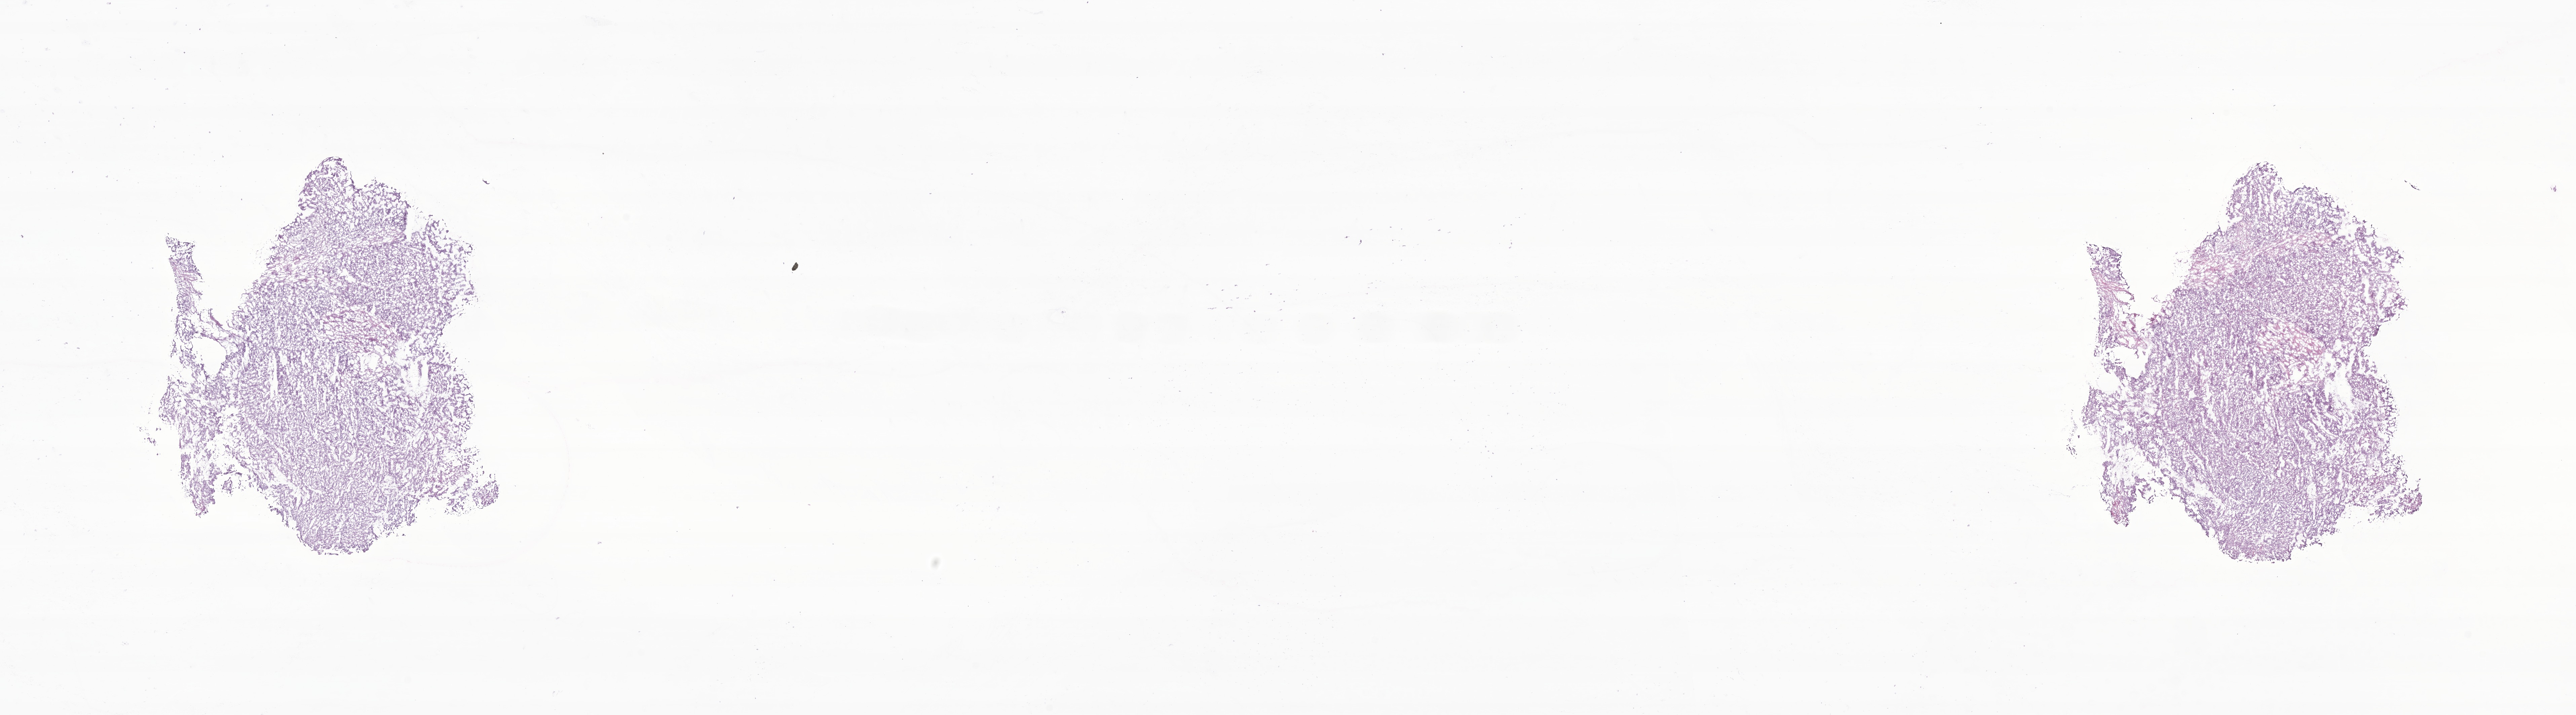
Digitized haematoxylin and eosin-stained section of tumor tissue from the colon — shown as a low-resolution overview of the whole scanned area (about 32.3 x 9.0 mm), frozen section (OCT-embedded). Patient: female, age 183 months.
• recorded diagnosis: Carcinoma, NOS